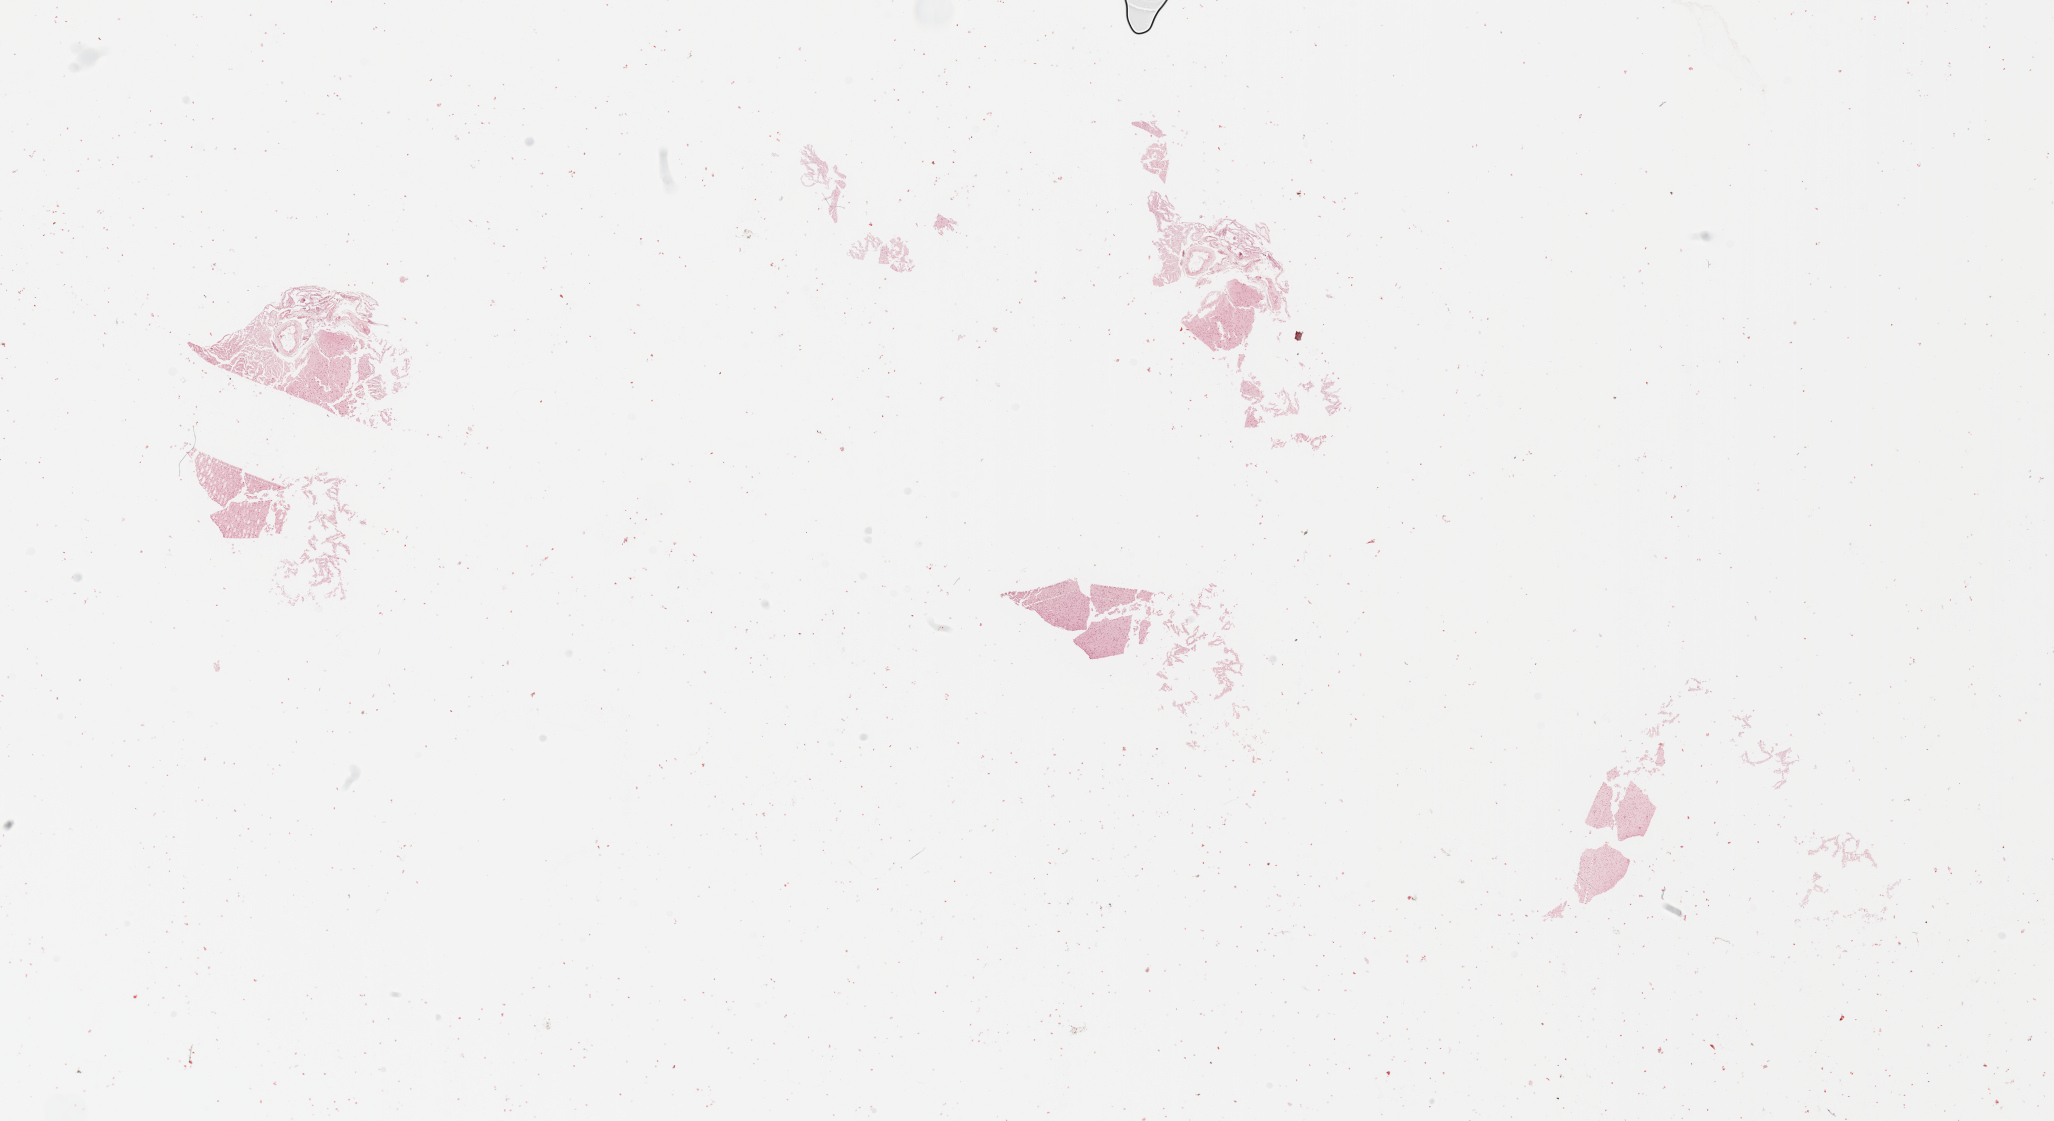
H&E whole-slide image — shown as a low-resolution overview of the whole scanned area (about 32.5 x 17.7 mm); tumour tissue sample, brain. 36-year-old female patient.
* patient diagnosis (cohort enrolment): glioblastoma multiforme (brain)
* primary tumour site (as recorded): temporal lobe